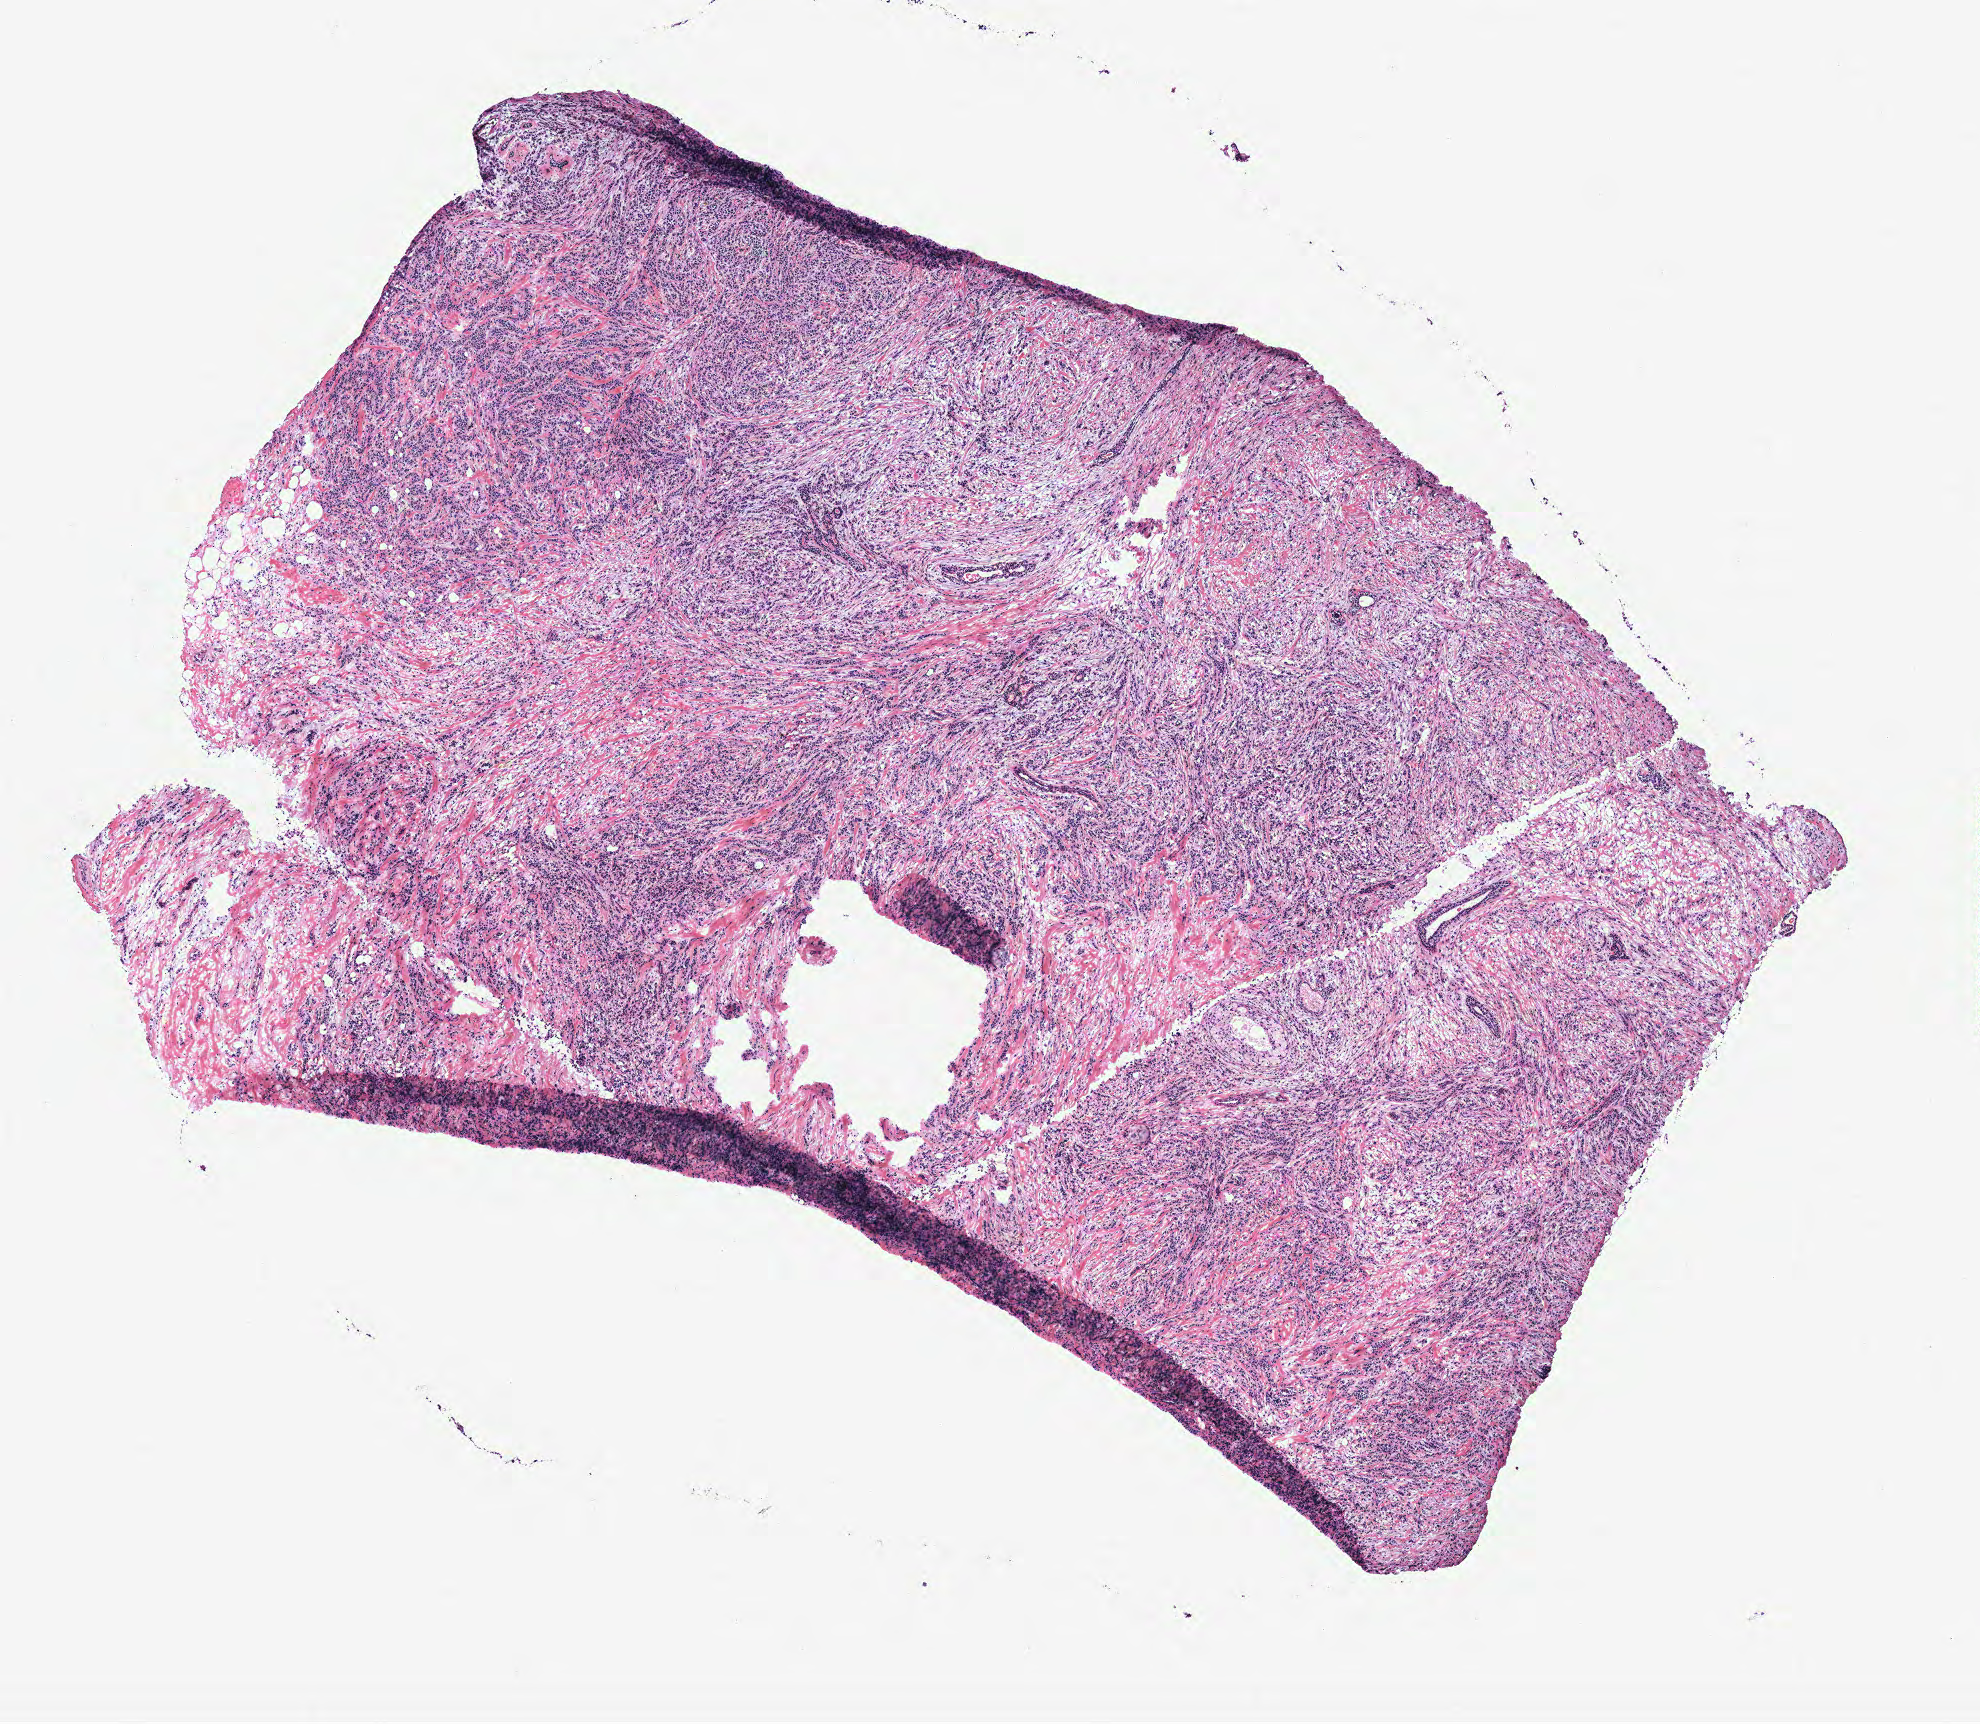
H&E-stained whole-slide image, low-resolution overview of the scanned area, about 7.9 x 6.9 mm; breast, tissue type not recorded. Patient: female, age 46 years.
Patient diagnosis: Infiltrating duct carcinoma, NOS.